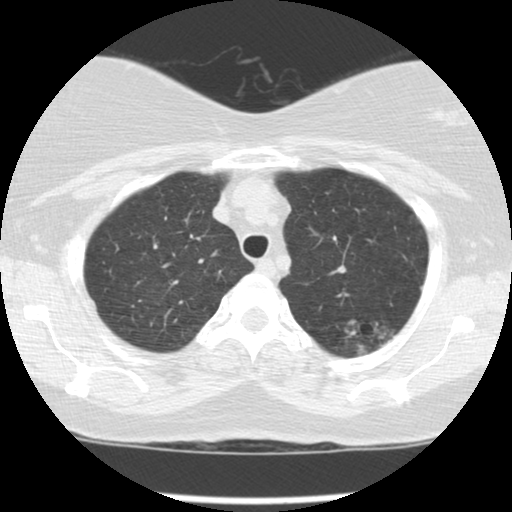
Axial slice from a low-dose chest CT screening exam. Third screening round (two years after baseline). Lung window (W 1500 / L -600 HU). 2.5 mm slice thickness. Standard (soft-tissue) reconstruction kernel (STANDARD). 120 kVp. 512 × 512 image matrix, field of view 310 × 310 mm. Female participant, aged 56 years at enrolment.
Expert reader's lesion annotation, bounding box [x1, y1, x2, y2] px = [334, 302, 408, 359]. The screening reader recorded 4 non-calcified nodules or masses ≥4 mm on this exam; which of them this box marks is not recorded. Official screen result: positive, other. Lung cancer was diagnosed 49 days after this screen: adenocarcinoma, NOS, left upper lobe, moderately differentiated (G2), stage IA (AJCC 6th edition), 10 mm at pathology.